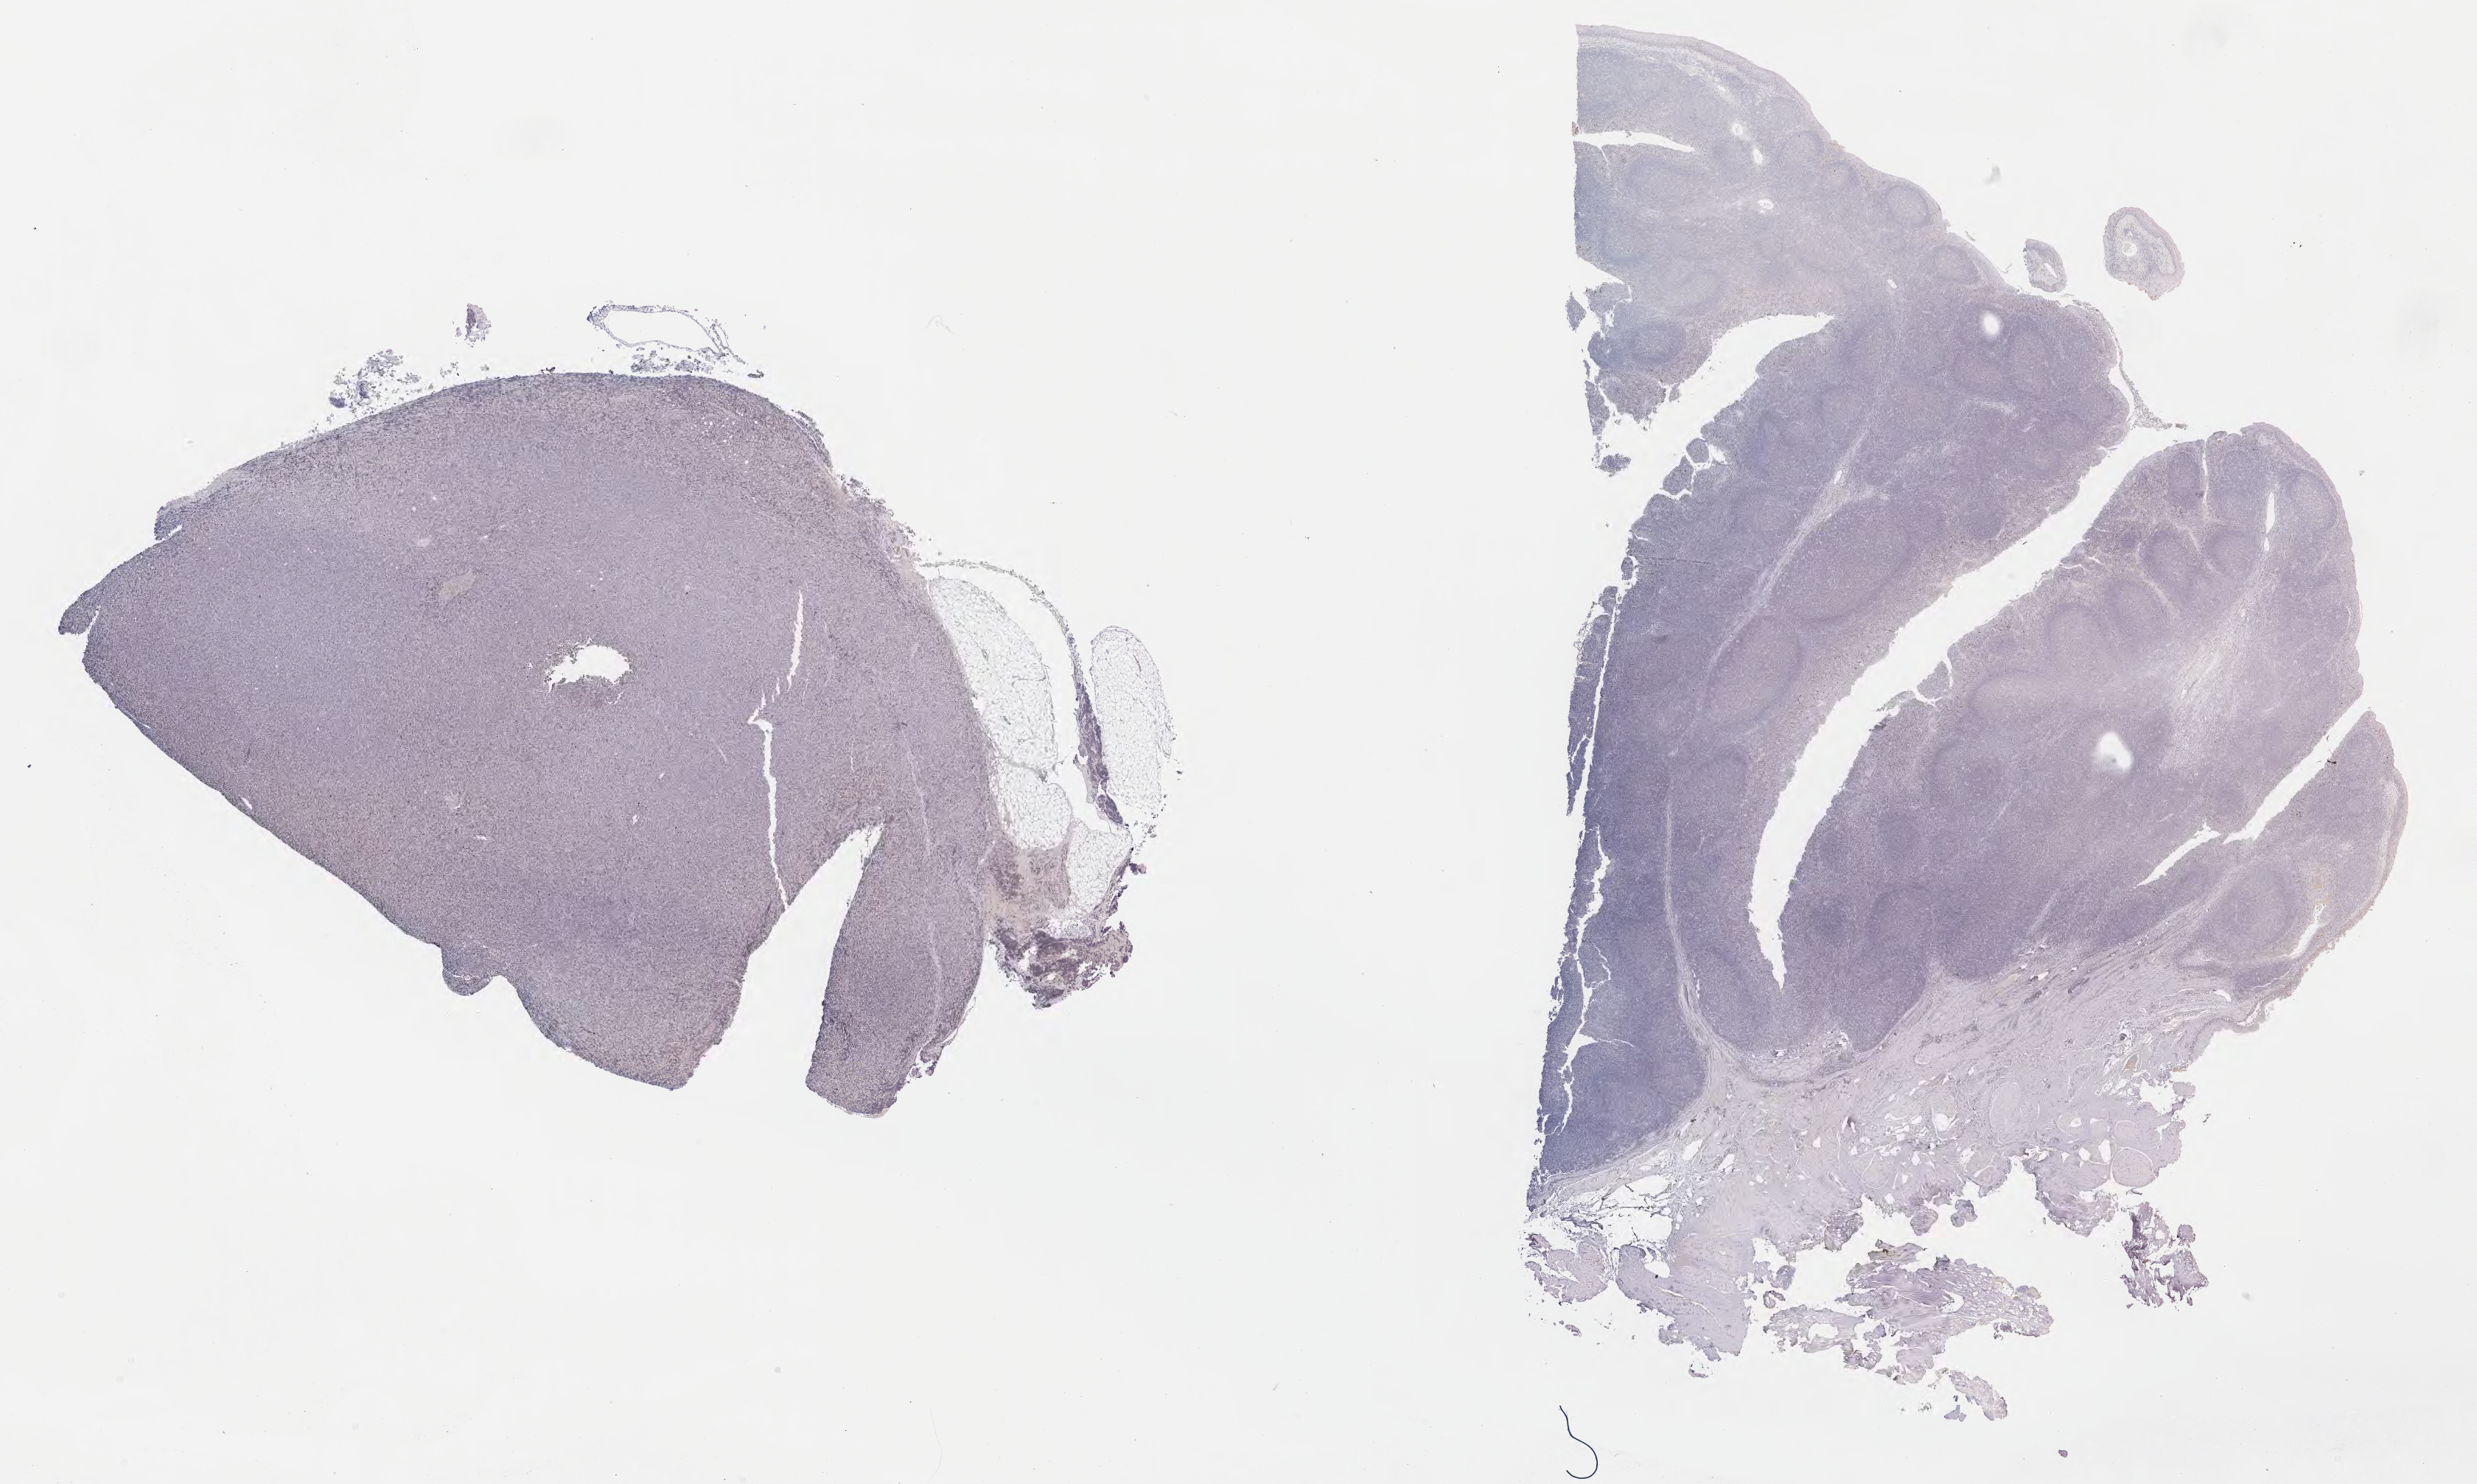
Whole-slide image, immunohistochemical stain for p53, a low-resolution overview of the entire scanned area, about 27.2 x 16.3 mm; specimen: tumor tissue; anatomic site: lymph node. Male patient, aged 26.
Histologic diagnosis: Diffuse large B-cell lymphoma, NOS.